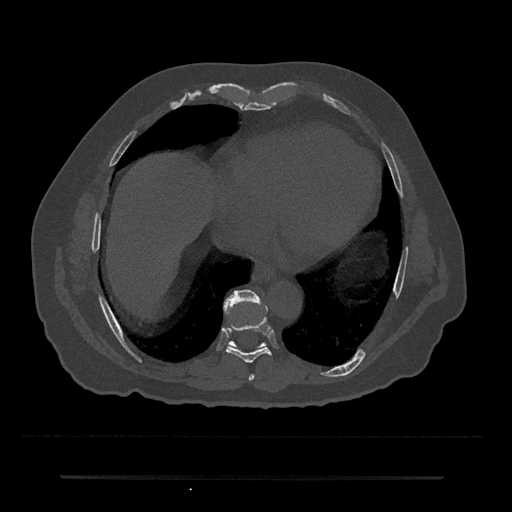
CT including the spine, one axial slice. Slice 318 of 797 in the series (ordered by position). Reconstruction kernel Br40s/3. 120 kVp. Bone window (W 1800 / L 400 HU). 0.5 mm slice thickness. 512 × 512 image matrix, field of view 437 × 437 mm. Patient: male, 69 years. From the clinical record (not read from this slice): primary cancer: prostate.
Structures marked on this image (semi-automatic segmentation, software-assisted and operator-edited):
- T7 vertebra: box from (x=248, y=374) to (x=255, y=381) px
- T8 vertebra: (x=226, y=317)–(x=272, y=363)
- T9 vertebra: (x=225, y=290)–(x=261, y=344)